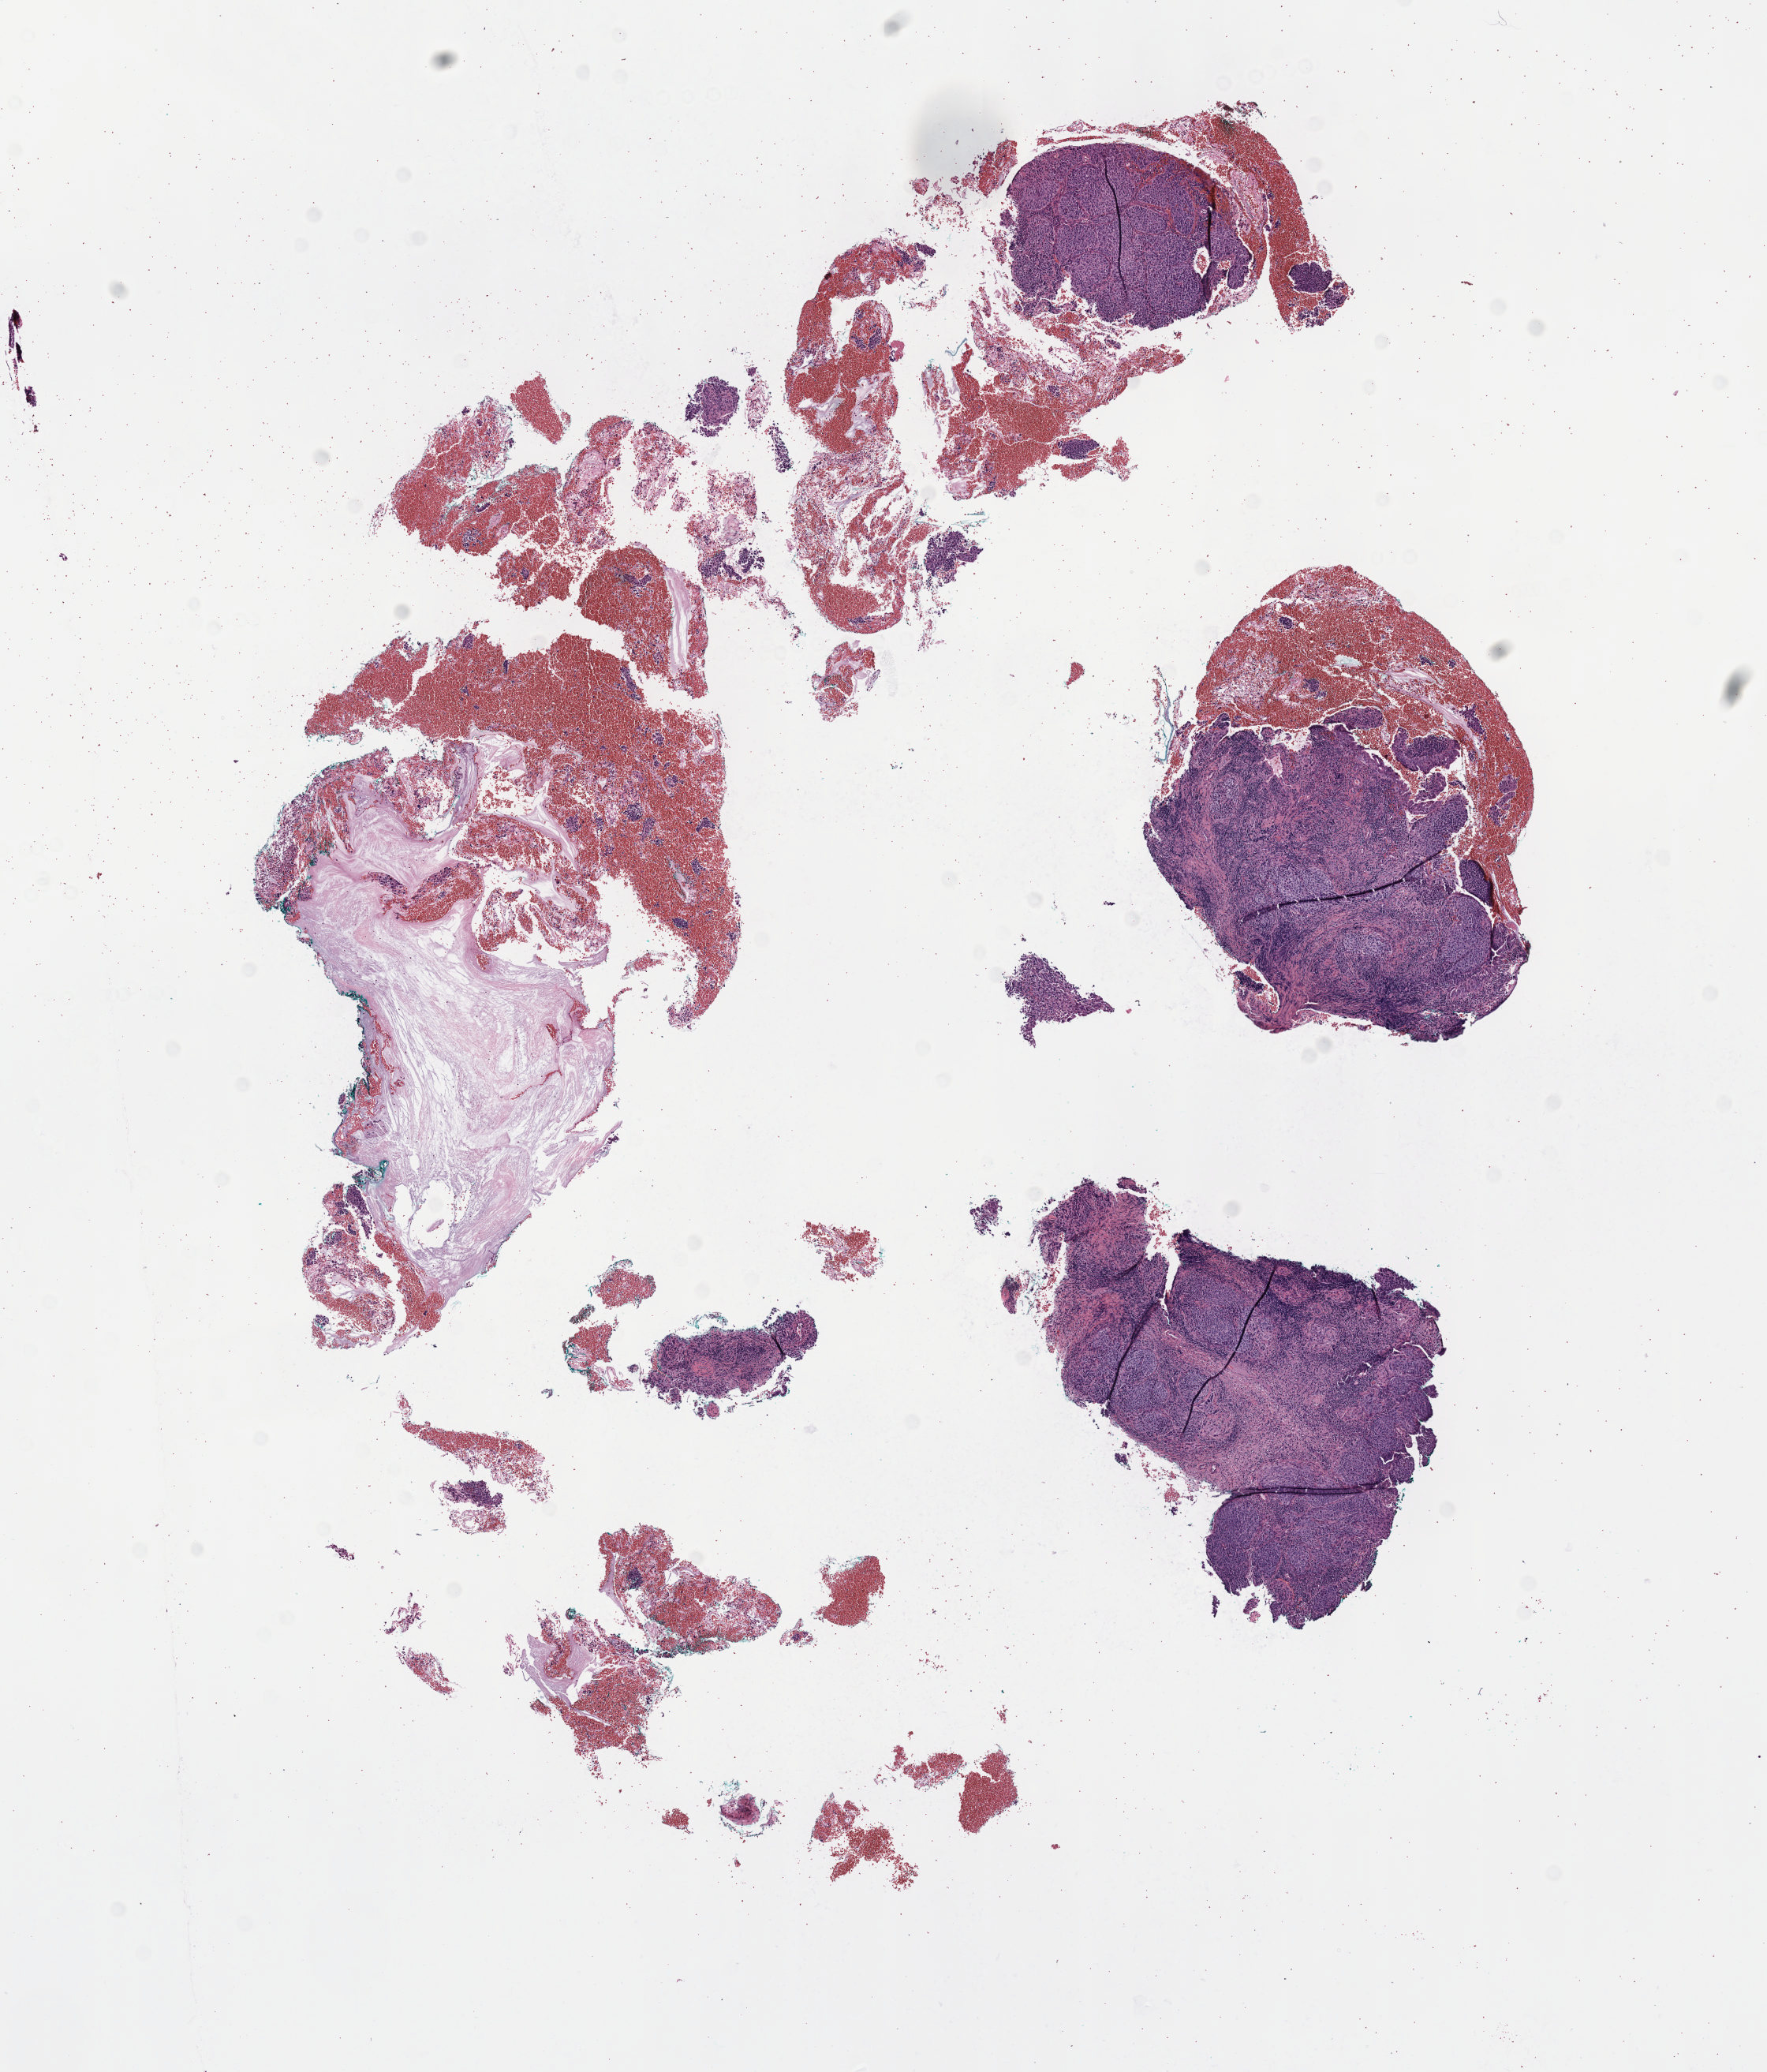
Digitized Hematoxylin and eosin (H&E) stained tissue section (whole slide), whole scanned area (about 9.1 x 10.6 mm, slide scanned at 40x) shown as a low-resolution overview; formalin-fixed paraffin-embedded (FFPE) diagnostic section; sample: primary tumour, cervix. Female patient; age at initial diagnosis 29 years. Histologic grade: G2 (moderately differentiated).
Lymph nodes positive (case pathology): 0 of 26 examined. Pathologic diagnosis: Squamous cell carcinoma, NOS (cervix uteri). FIGO stage: IB1.